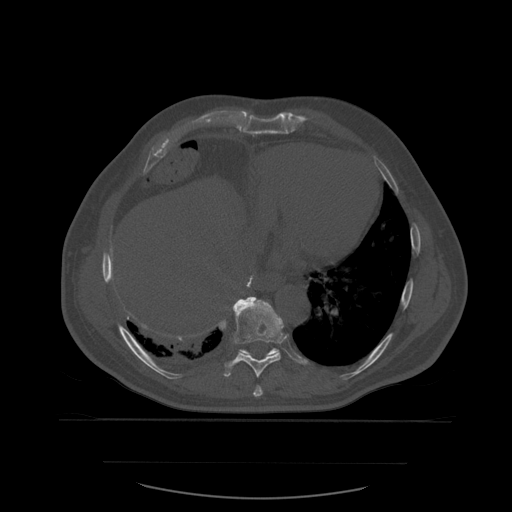
CT including the spine, one axial slice; position 336 of 590 along the scan axis; bone window (W 1800 / L 400 HU); 1.25 mm slice thickness; 512 × 512 image matrix, field of view 479 × 479 mm. Patient age 71 years. From the clinical record (not read from this slice): primary cancer: lung; vertebrae with lytic lesions (as recorded): T1, T2, L5, S1.
Annotated regions visible in this slice (semi-automatically segmented with operator editing):
- T10 vertebra: bounding box <235,297,285,356> (left, top, right, bottom; pixels)
- T8 vertebra: <253,386,264,397>
- T9 vertebra: <222,297,284,378>